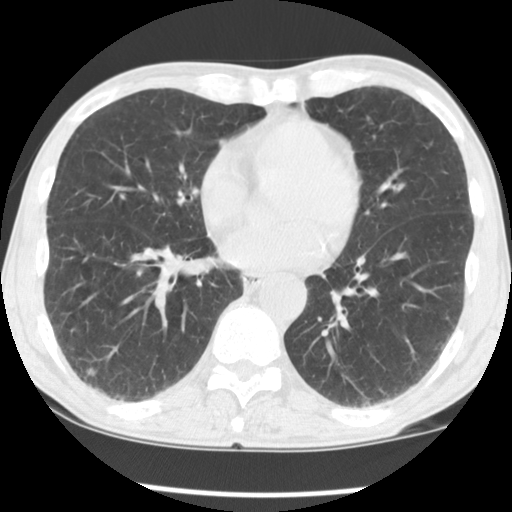
Low-dose screening chest CT, one axial slice; slice 56 of 135 in the series (ordered by position); 120 kVp; lung window (W 1500 / L -600 HU); 2.5 mm slice thickness; 512 × 512 image matrix.
Annotated regions visible in this slice (outlined manually by an expert reader):
- lesion 1 (tumor, lower lobe of right lung): bounding box <87,368,96,376> (left, top, right, bottom; pixels)